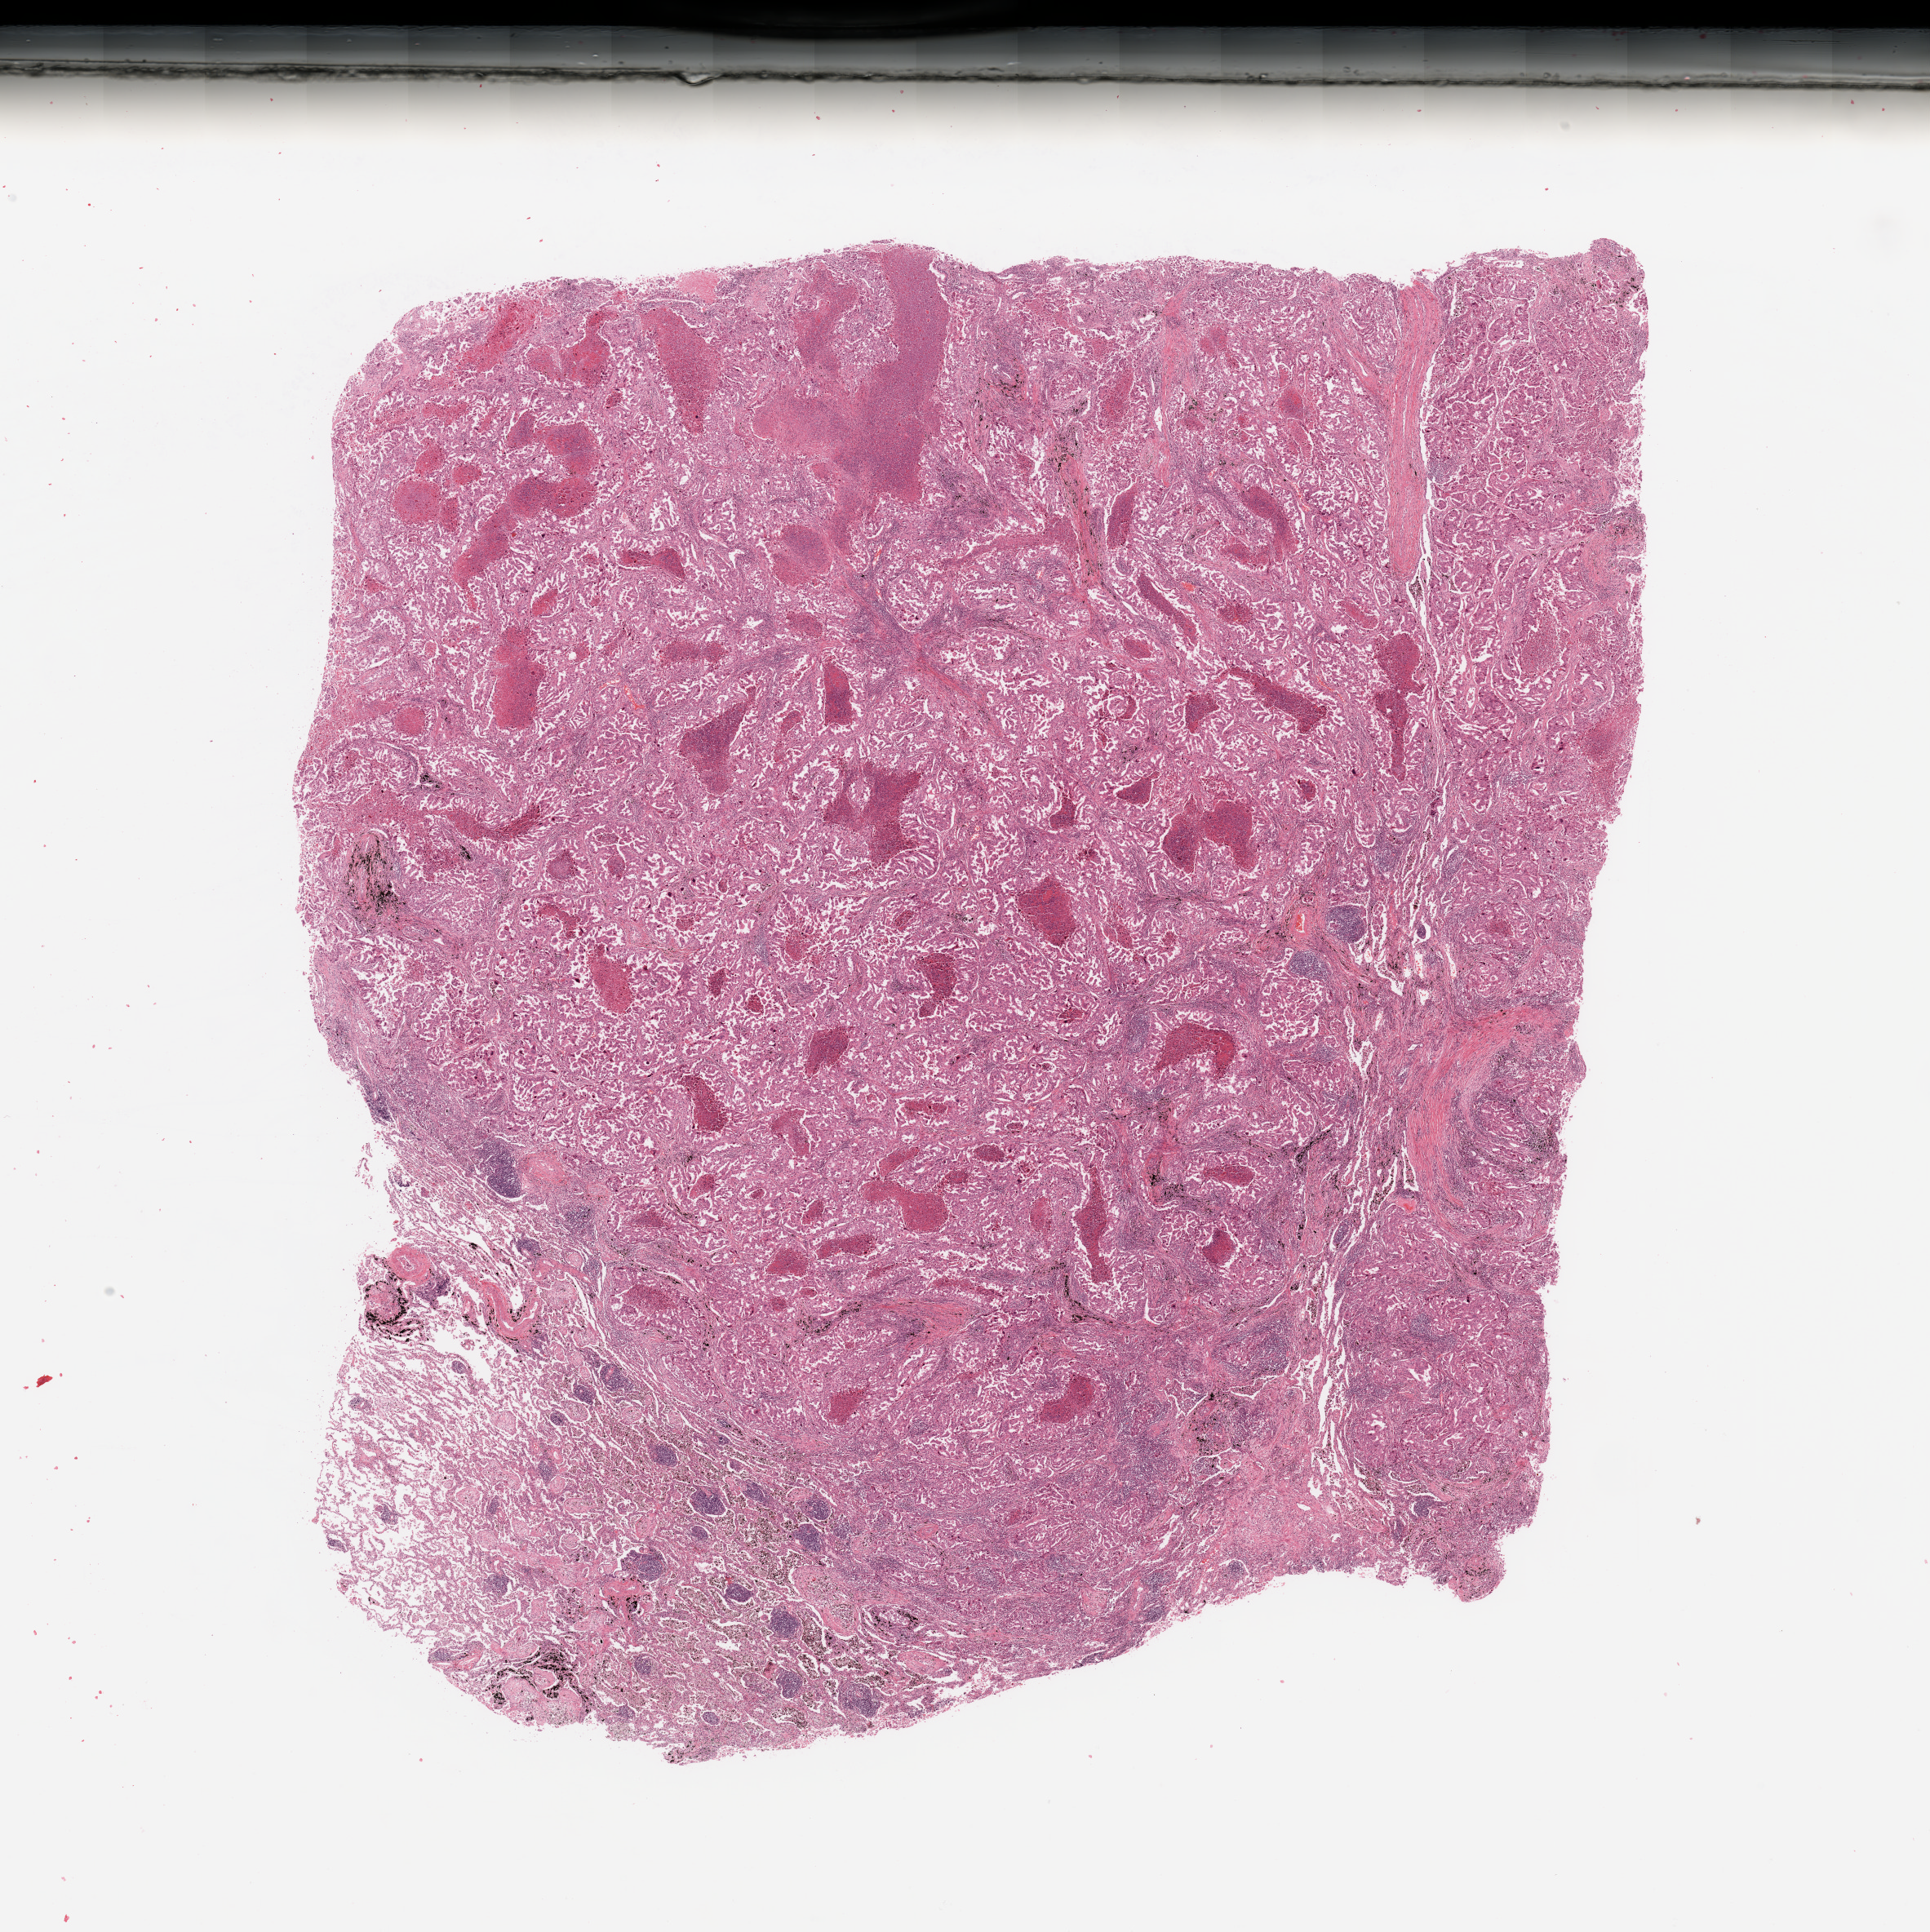
Digitized H&E tissue section (whole slide) — a low-resolution overview of the entire scanned area, about 18.7 x 18.7 mm (acquisition: 20x scan); lung, tumour tissue. Patient: male, age 54 years. Histologic grade: G2 (moderately differentiated).
* histologic diagnosis: Adenocarcinoma, NOS
* AJCC pathologic stage: IB